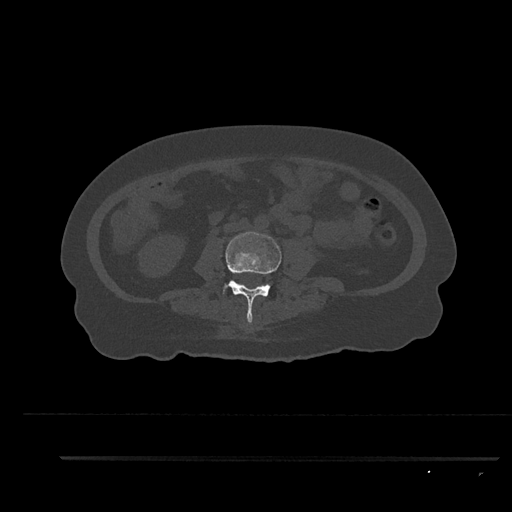
CT including the spine, one axial slice. Position 79 of 797 along the scan axis. Reconstruction kernel Br40s/3. 120 kVp. Bone window (W 1800 / L 400 HU). 0.5 mm slice thickness. 512 × 512 image matrix, field of view 408 × 408 mm. Female patient, age 44 years. From the clinical record (not read from this slice): primary cancer: renal; vertebrae with lytic lesions (as recorded): L1.
Outlined on this slice (semi-automatic segmentation, software-assisted and operator-edited):
- L3 vertebra: box from (x=223, y=231) to (x=282, y=323) px